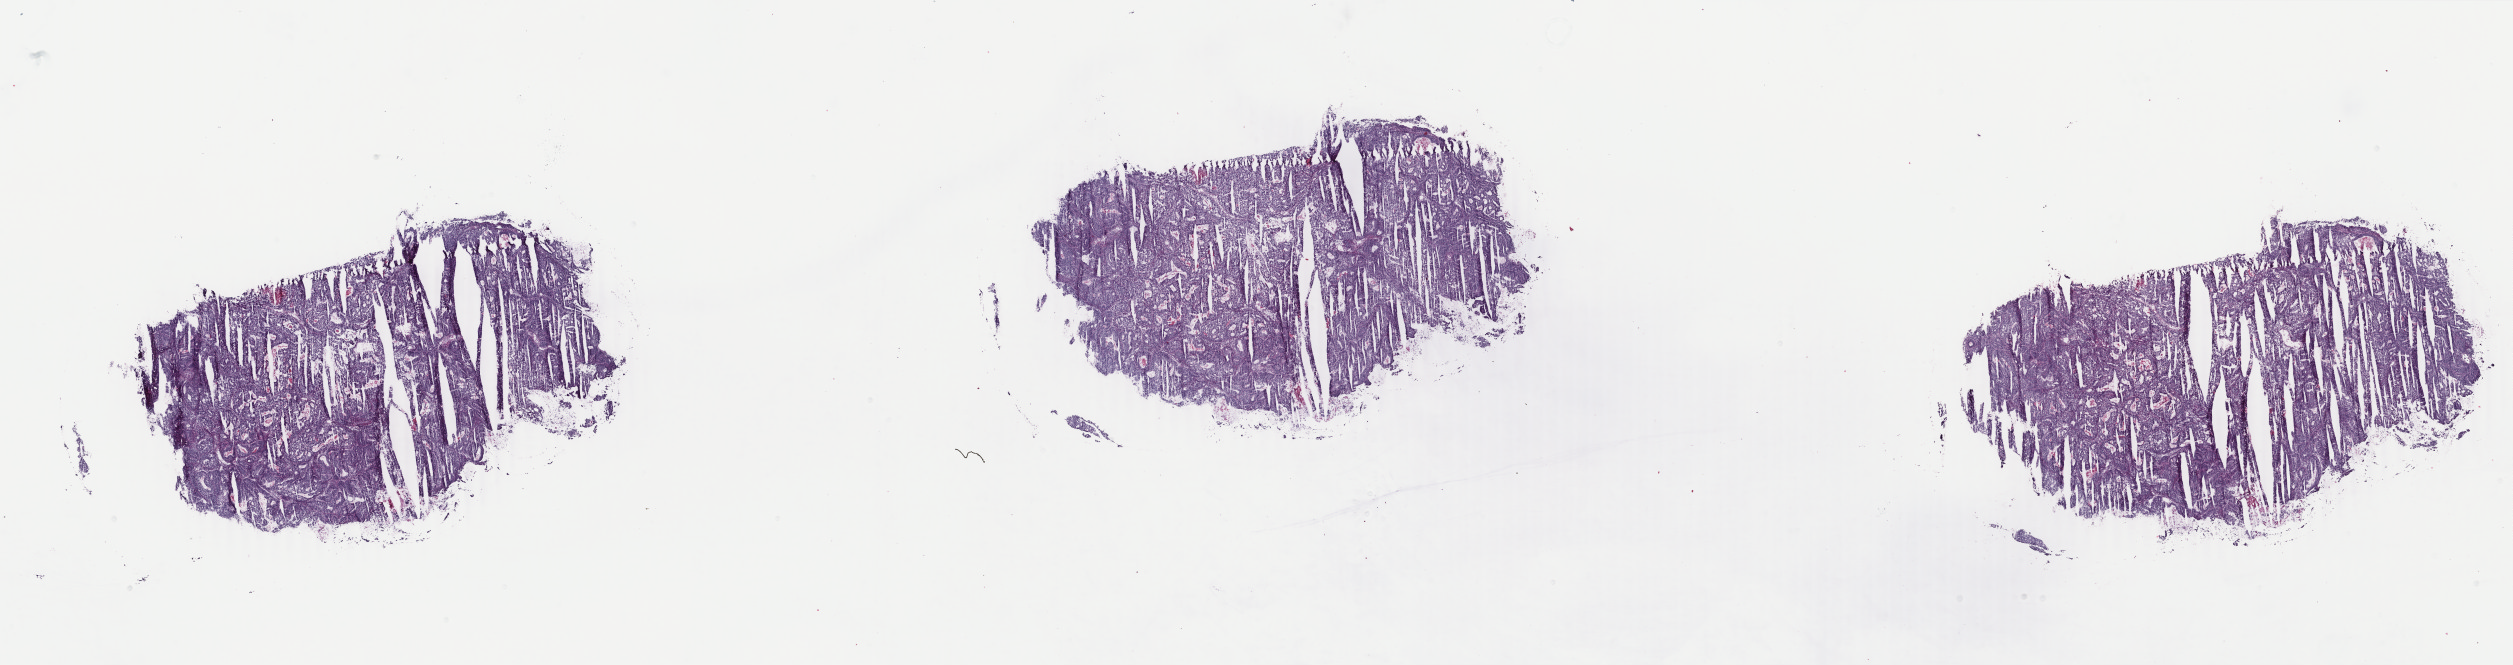
Whole-slide histology image, H&E — shown as a low-resolution overview of the whole scanned area (about 40.0 x 10.6 mm); frozen section from the top of the tissue portion; sample: primary tumour, uterus. Female, age 44 years at initial diagnosis. Histologic grade: G2 (moderately differentiated). Pathologist review of this section (percent, as recorded): tumour cells 60%, tumour nuclei 70%, normal cells 30%, stromal cells 0%, necrosis 10%. Inflammatory infiltration, as recorded: lymphocyte infiltration 10%, monocyte infiltration 0%, neutrophil infiltration 5%.
* FIGO stage: IA
* histologic diagnosis: Endometrioid adenocarcinoma, NOS (endometrium)